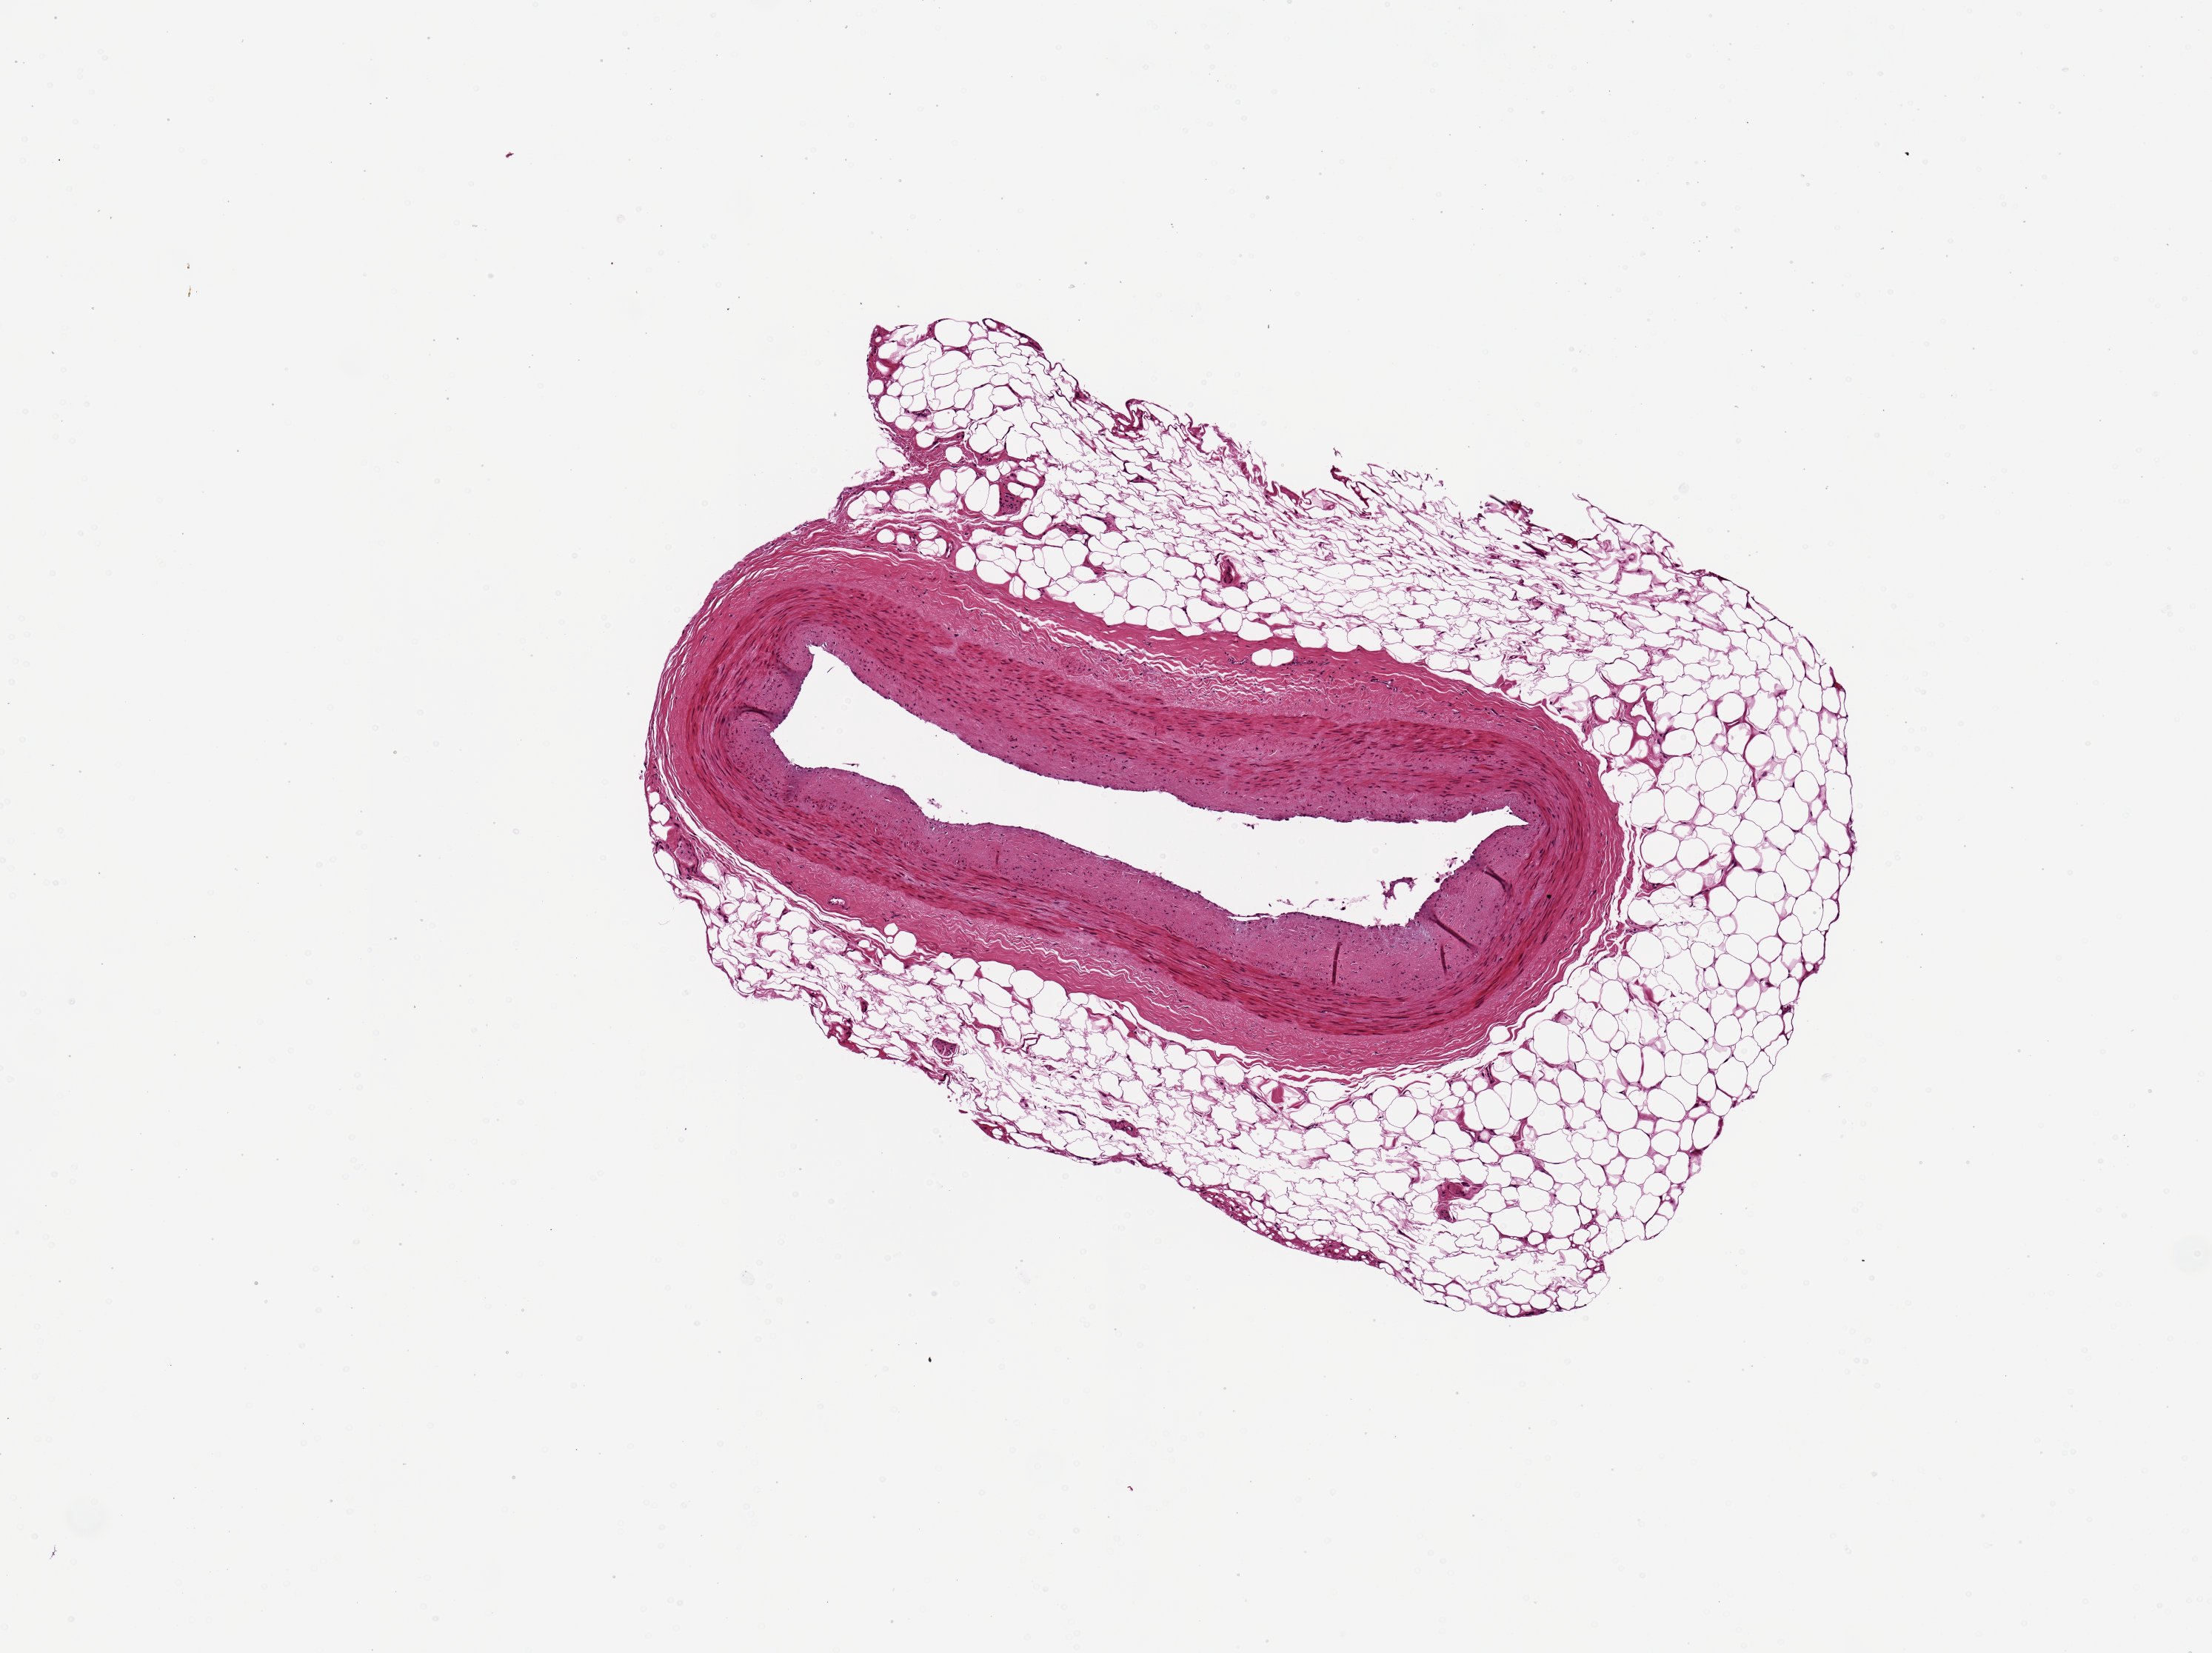
Digitized haematoxylin and eosin-stained section — low-resolution overview of the scanned area, about 5.9 x 4.4 mm (from a 20x scan); PAXgene-fixed, paraffin-embedded tissue; target tissue: coronary artery; donor tissue sample. Donor sex: male.
* reviewer comment on this tissue sample: About 40% fat in aliquot. 30% intimal sclerosis